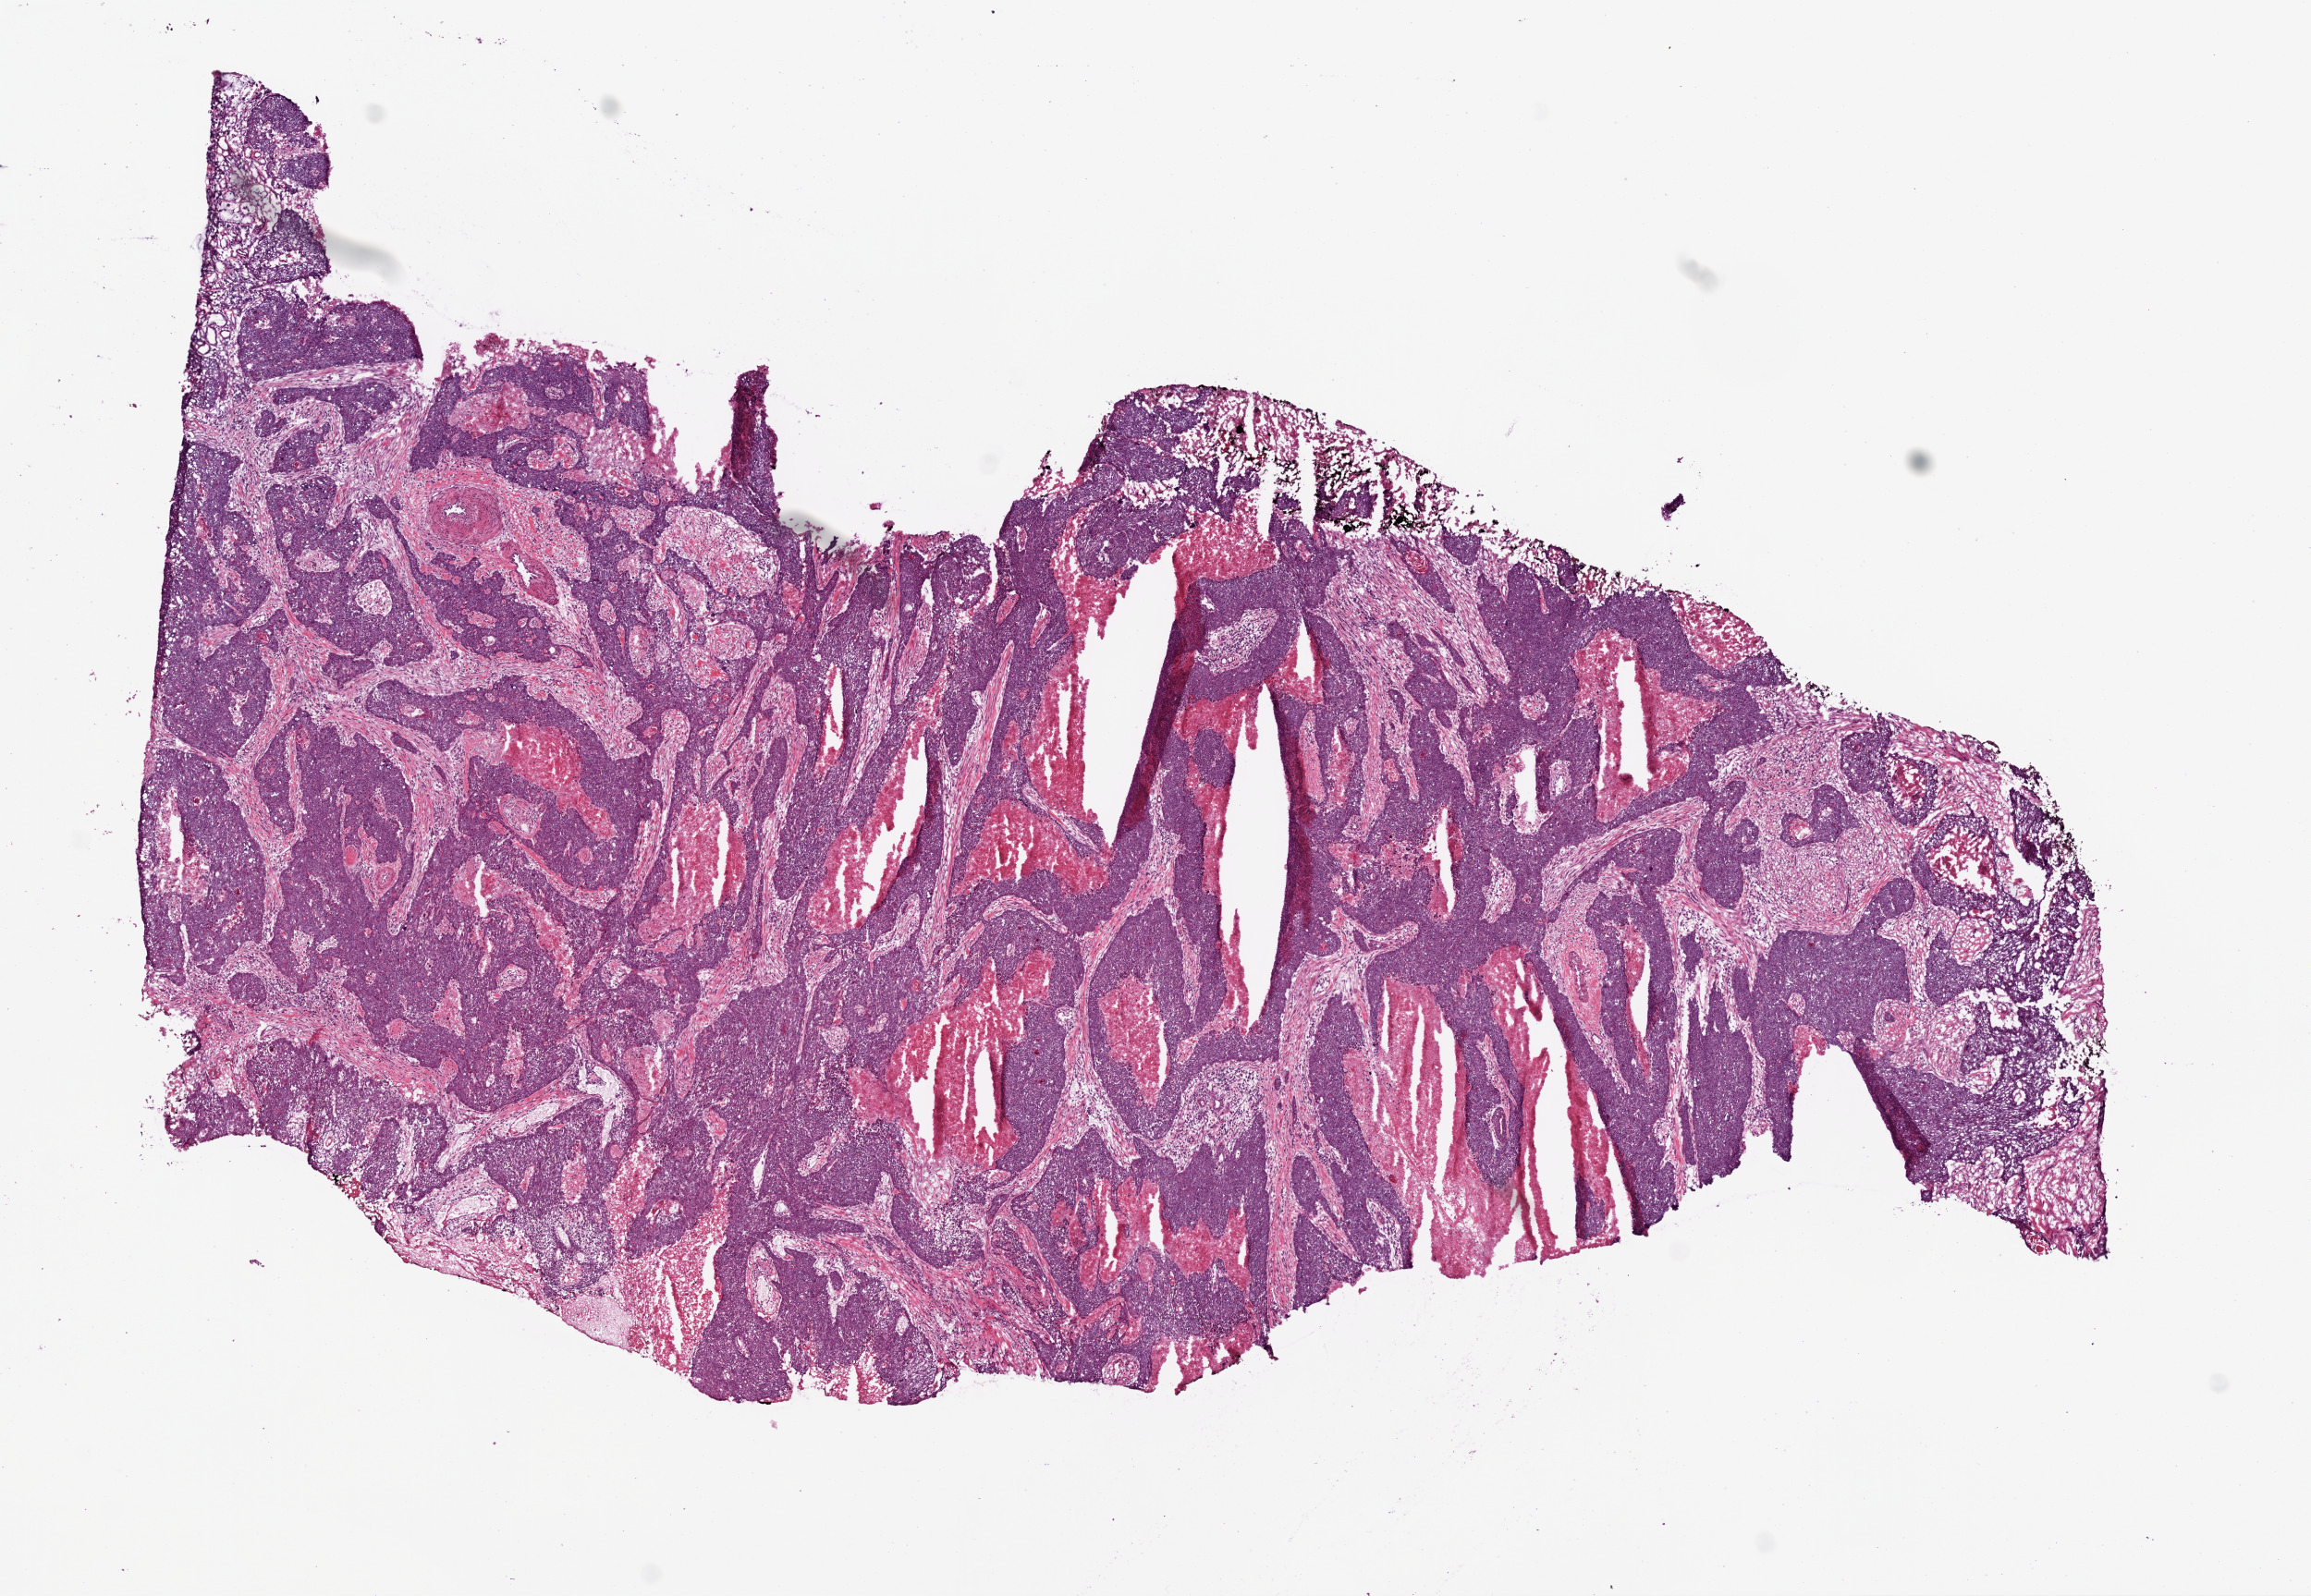
Whole-slide histology image, H&E-stained — low-resolution overview of the scanned area, about 10.0 x 6.9 mm (slide scanned at 20x). Frozen section from the bottom of the tissue portion. Head and neck, primary tumour sample. Patient: male, age at initial diagnosis 50 years. Histologic grade: GX (grade cannot be assessed). Pathologist review of this section (percent, as recorded): tumour cells 77%, tumour nuclei 90%, normal cells 0%, stromal cells 1%, necrosis 22%. Infiltration values recorded for this section: lymphocyte infiltration 2%.
* histologic diagnosis: Squamous cell carcinoma, NOS (base of tongue, NOS)
* AJCC pathologic stage: III (7th edition)
* TNM: T3 NX